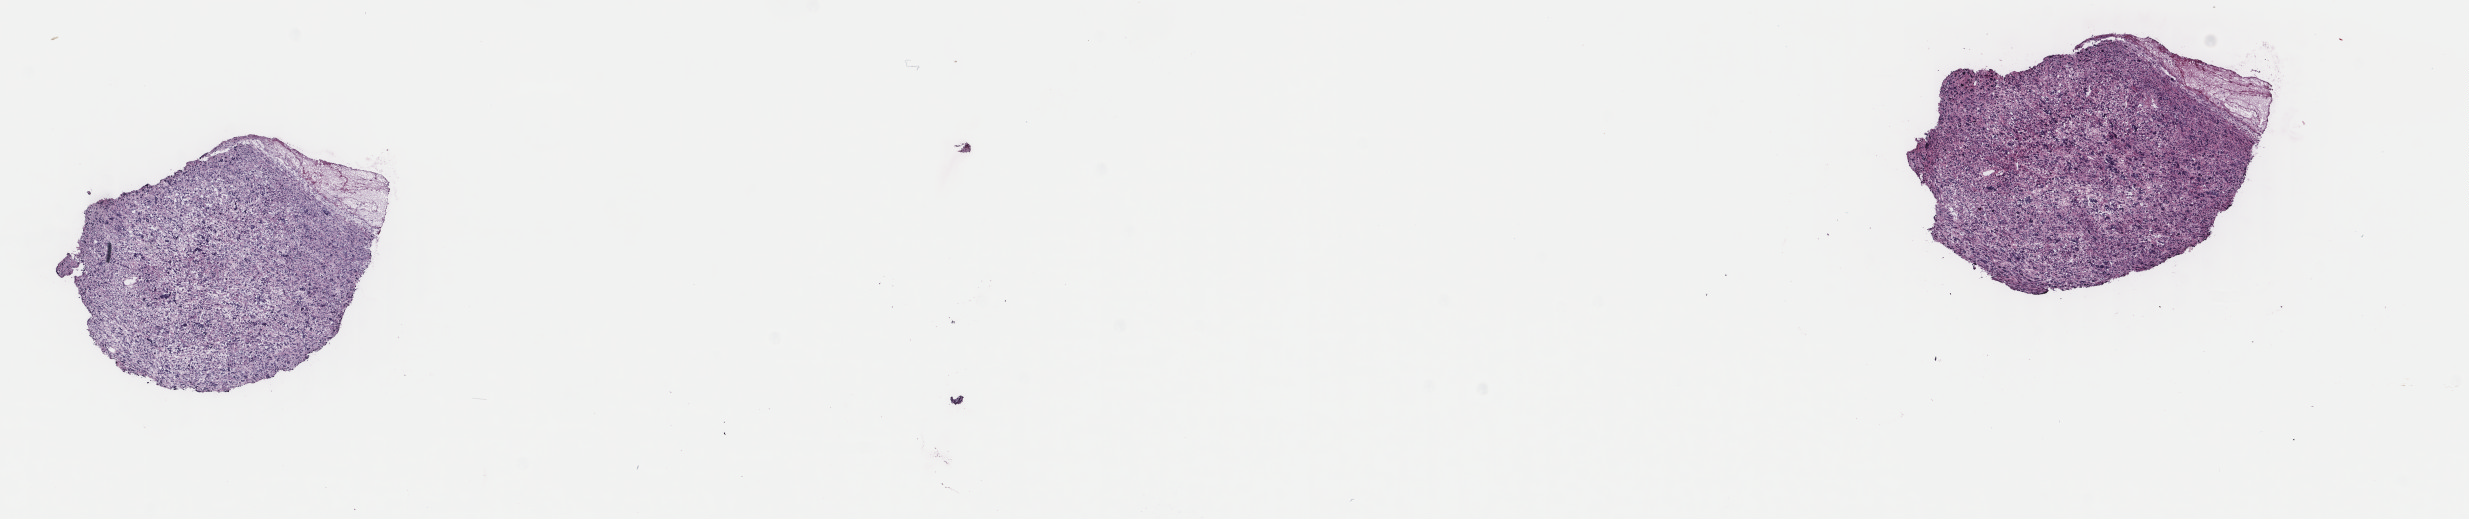
Digitized H&E tissue section (whole slide) — low-resolution overview of the scanned area, about 19.6 x 4.1 mm (from a 40x scan), frozen section from the top of the tissue portion, primary tumour sample from the uterus. Patient: female, age at initial diagnosis 58 years. Composition of this section per pathologist review: tumour cells 80%, tumour nuclei 80%, normal cells 0%, stromal cells 20%, necrosis 0%. Infiltration values recorded for this section: lymphocyte infiltration 3%, monocyte infiltration 1%, neutrophil infiltration 1%.
Pathologic diagnosis: Leiomyosarcoma, NOS.